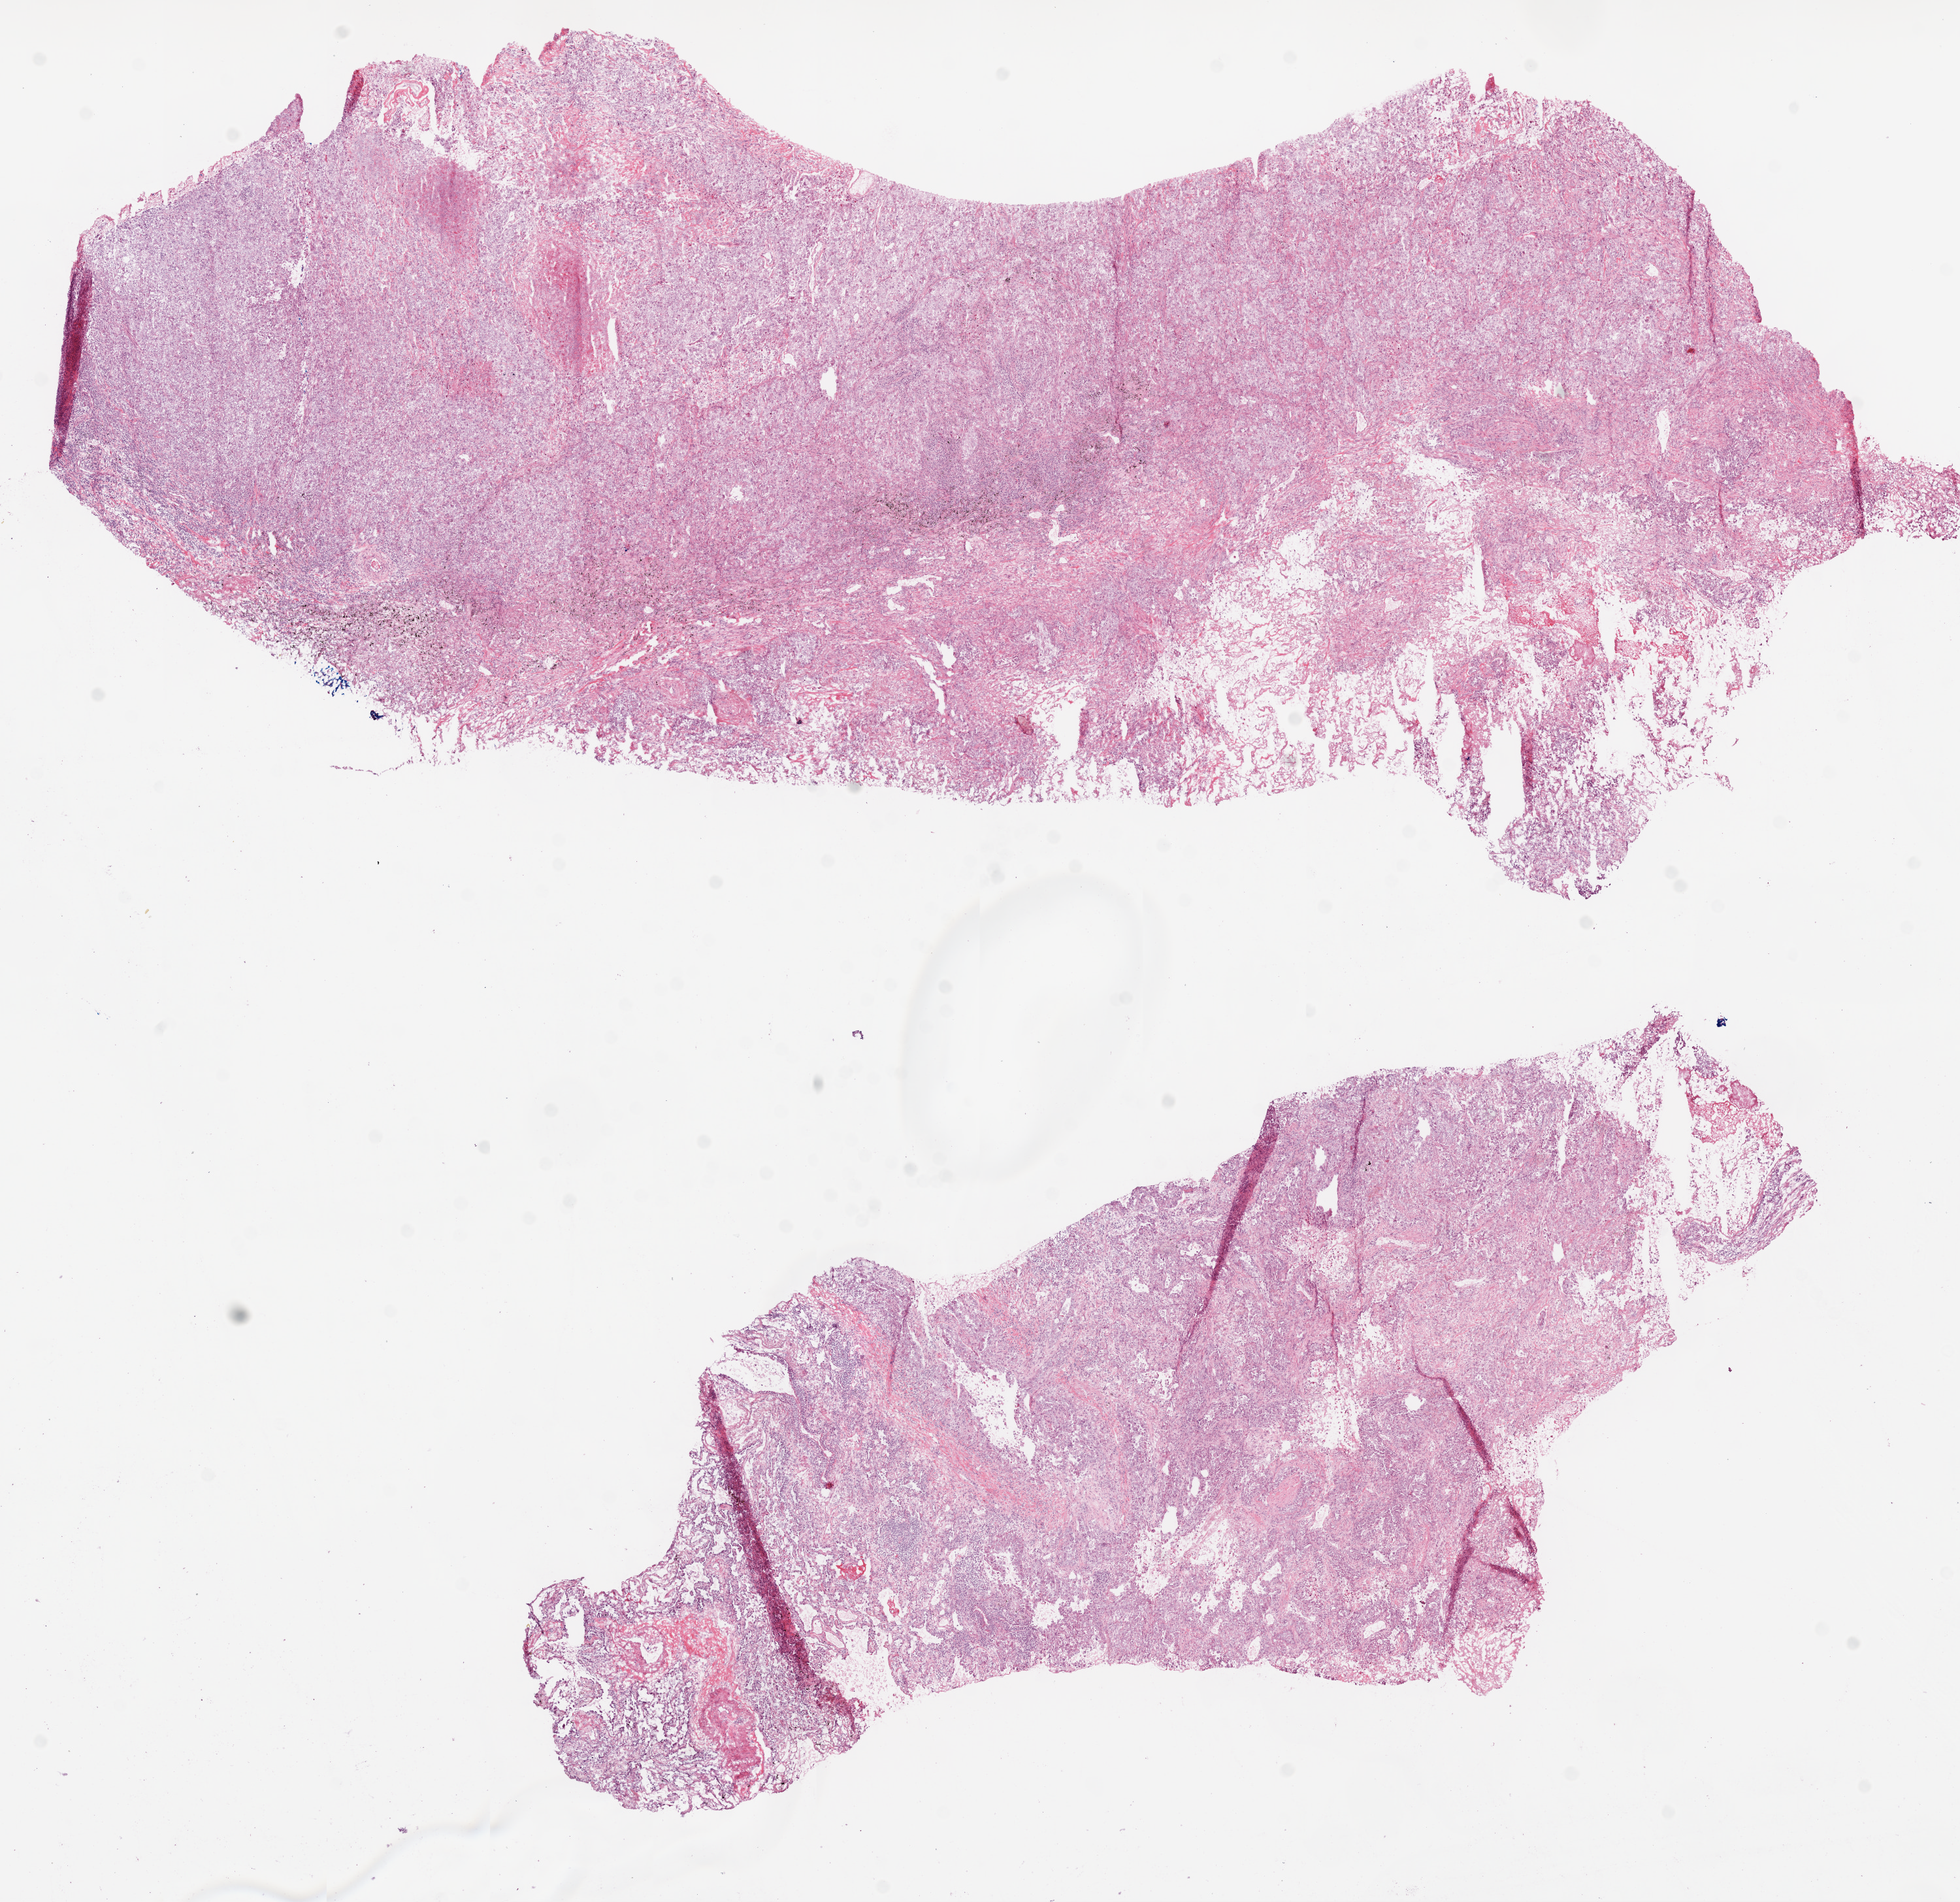
Digitized Hematoxylin and eosin (H&E) stained tissue section (whole slide) — low-resolution overview of the scanned area, about 12.0 x 11.7 mm (from a 20x scan). Frozen section. Lung, primary tumour sample. Male patient; age at initial diagnosis 68 years. Composition of this section per pathologist review: tumour cells 70%, tumour nuclei 70%, normal cells 10%, stromal cells 15%, necrosis 5%.
• diagnosis: Adenocarcinoma, NOS (upper lobe, lung)
• AJCC pathologic stage: IIB